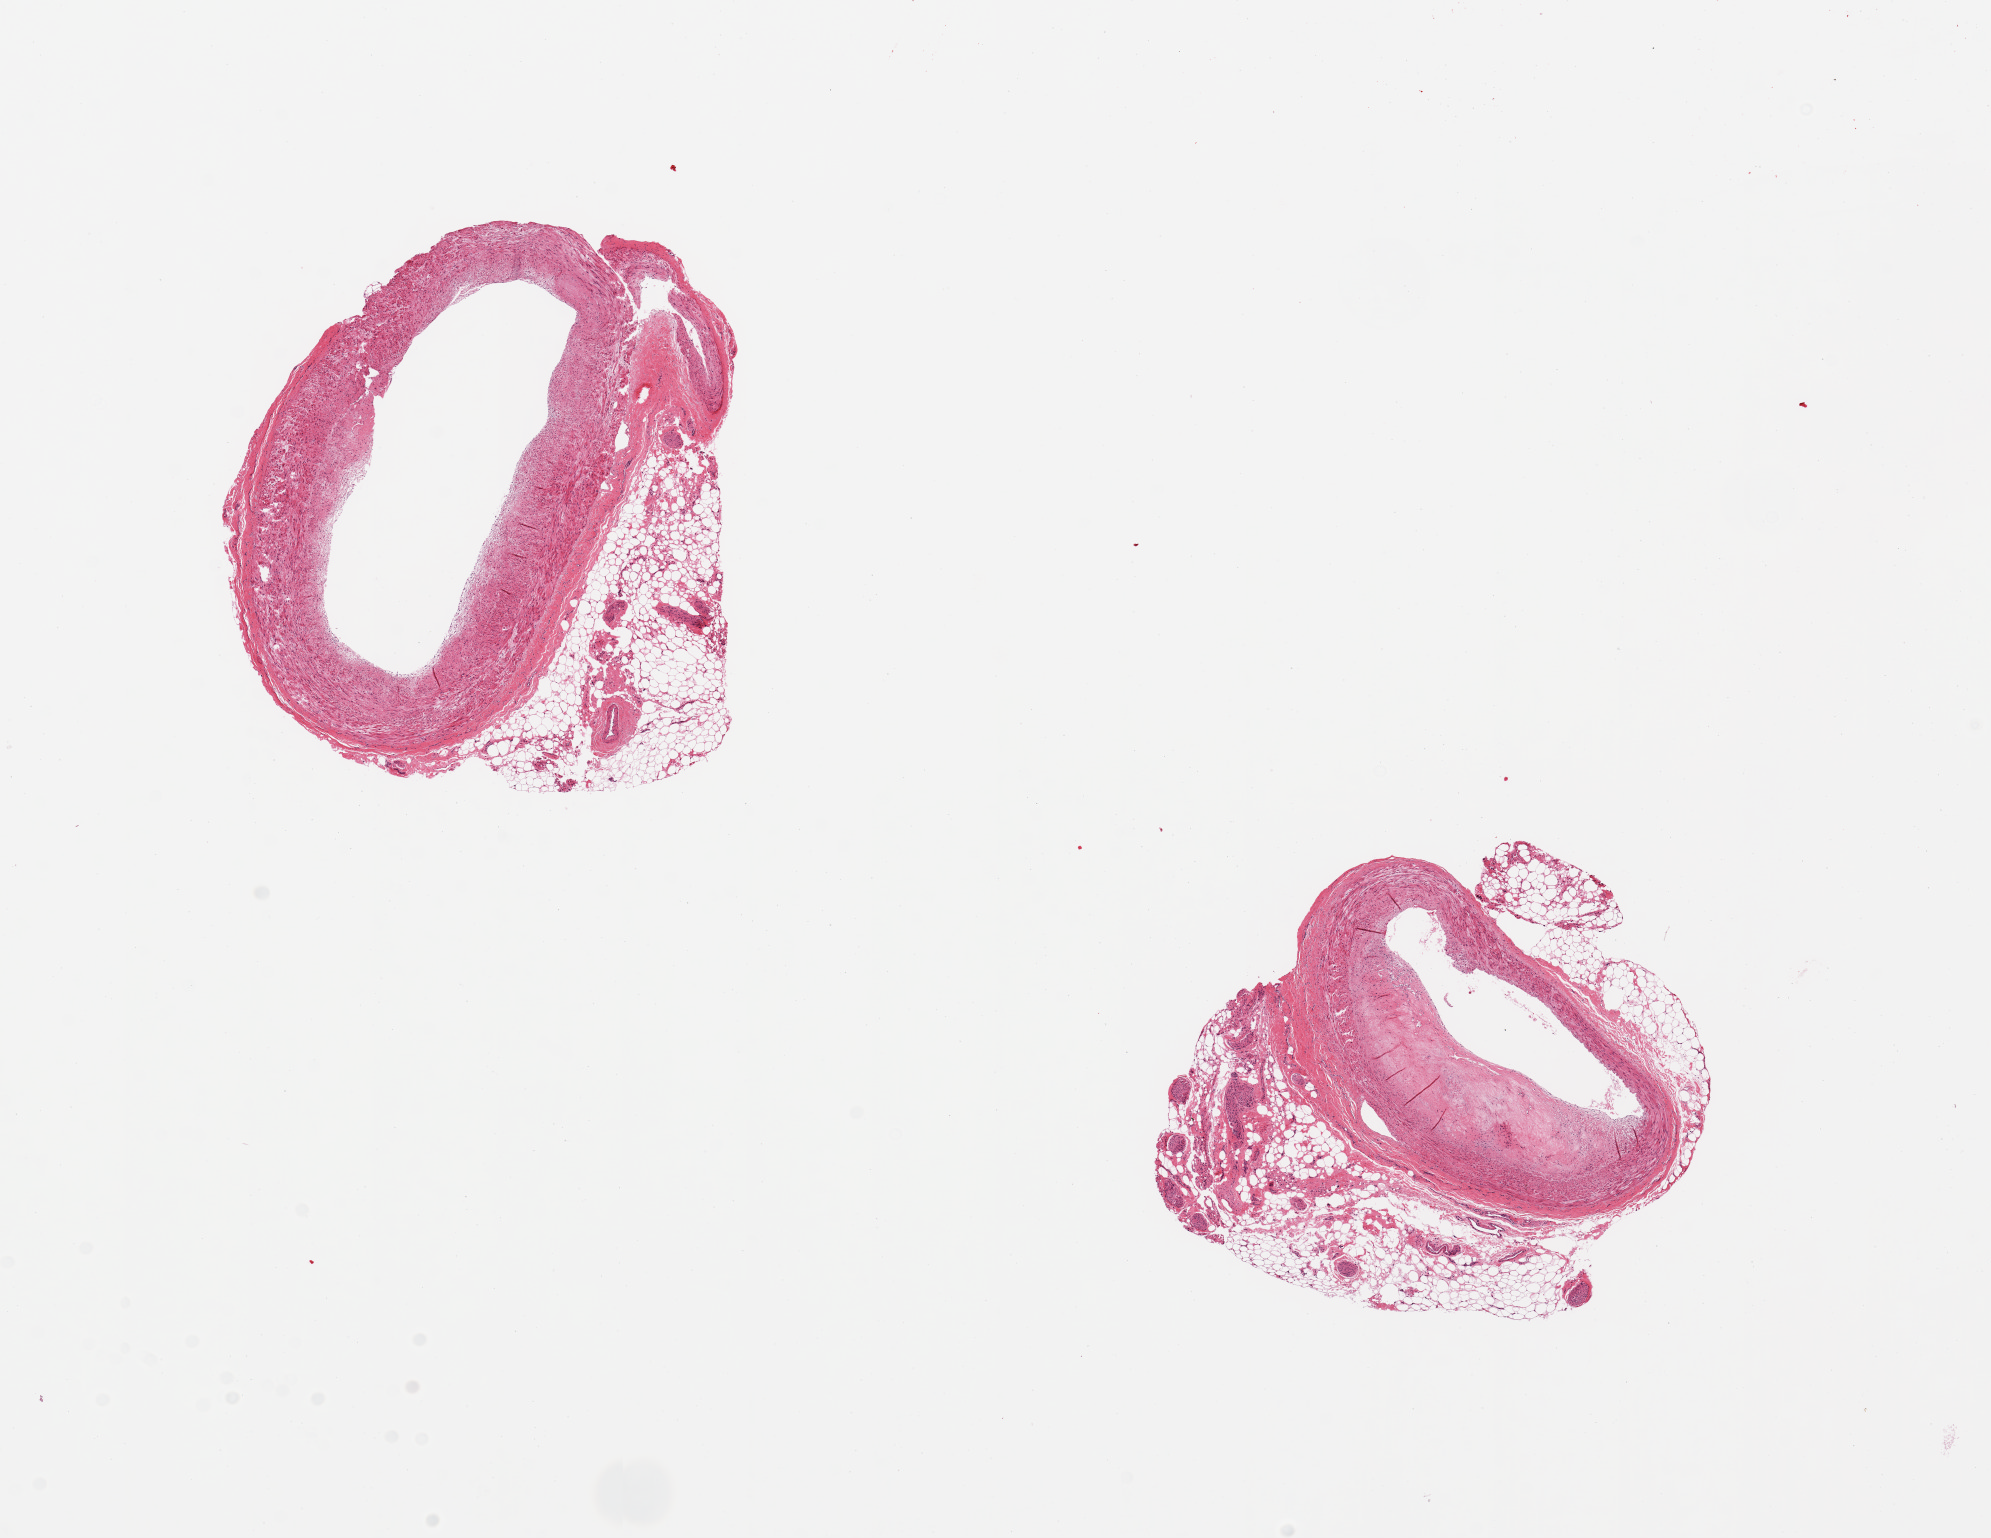
Whole-slide image, haematoxylin and eosin stain, whole scanned area (about 15.8 x 12.2 mm) shown as a low-resolution overview; PAXgene-fixed paraffin-embedded (PFPE) section; target tissue: coronary artery; donor tissue sample. Female donor.
Pathologist's review note for this sample: 2 pieces, both with attachment of adipose tissue and nerve up to 1.45mm thick, atherosclerosis with compromise of the lumen ~40%.